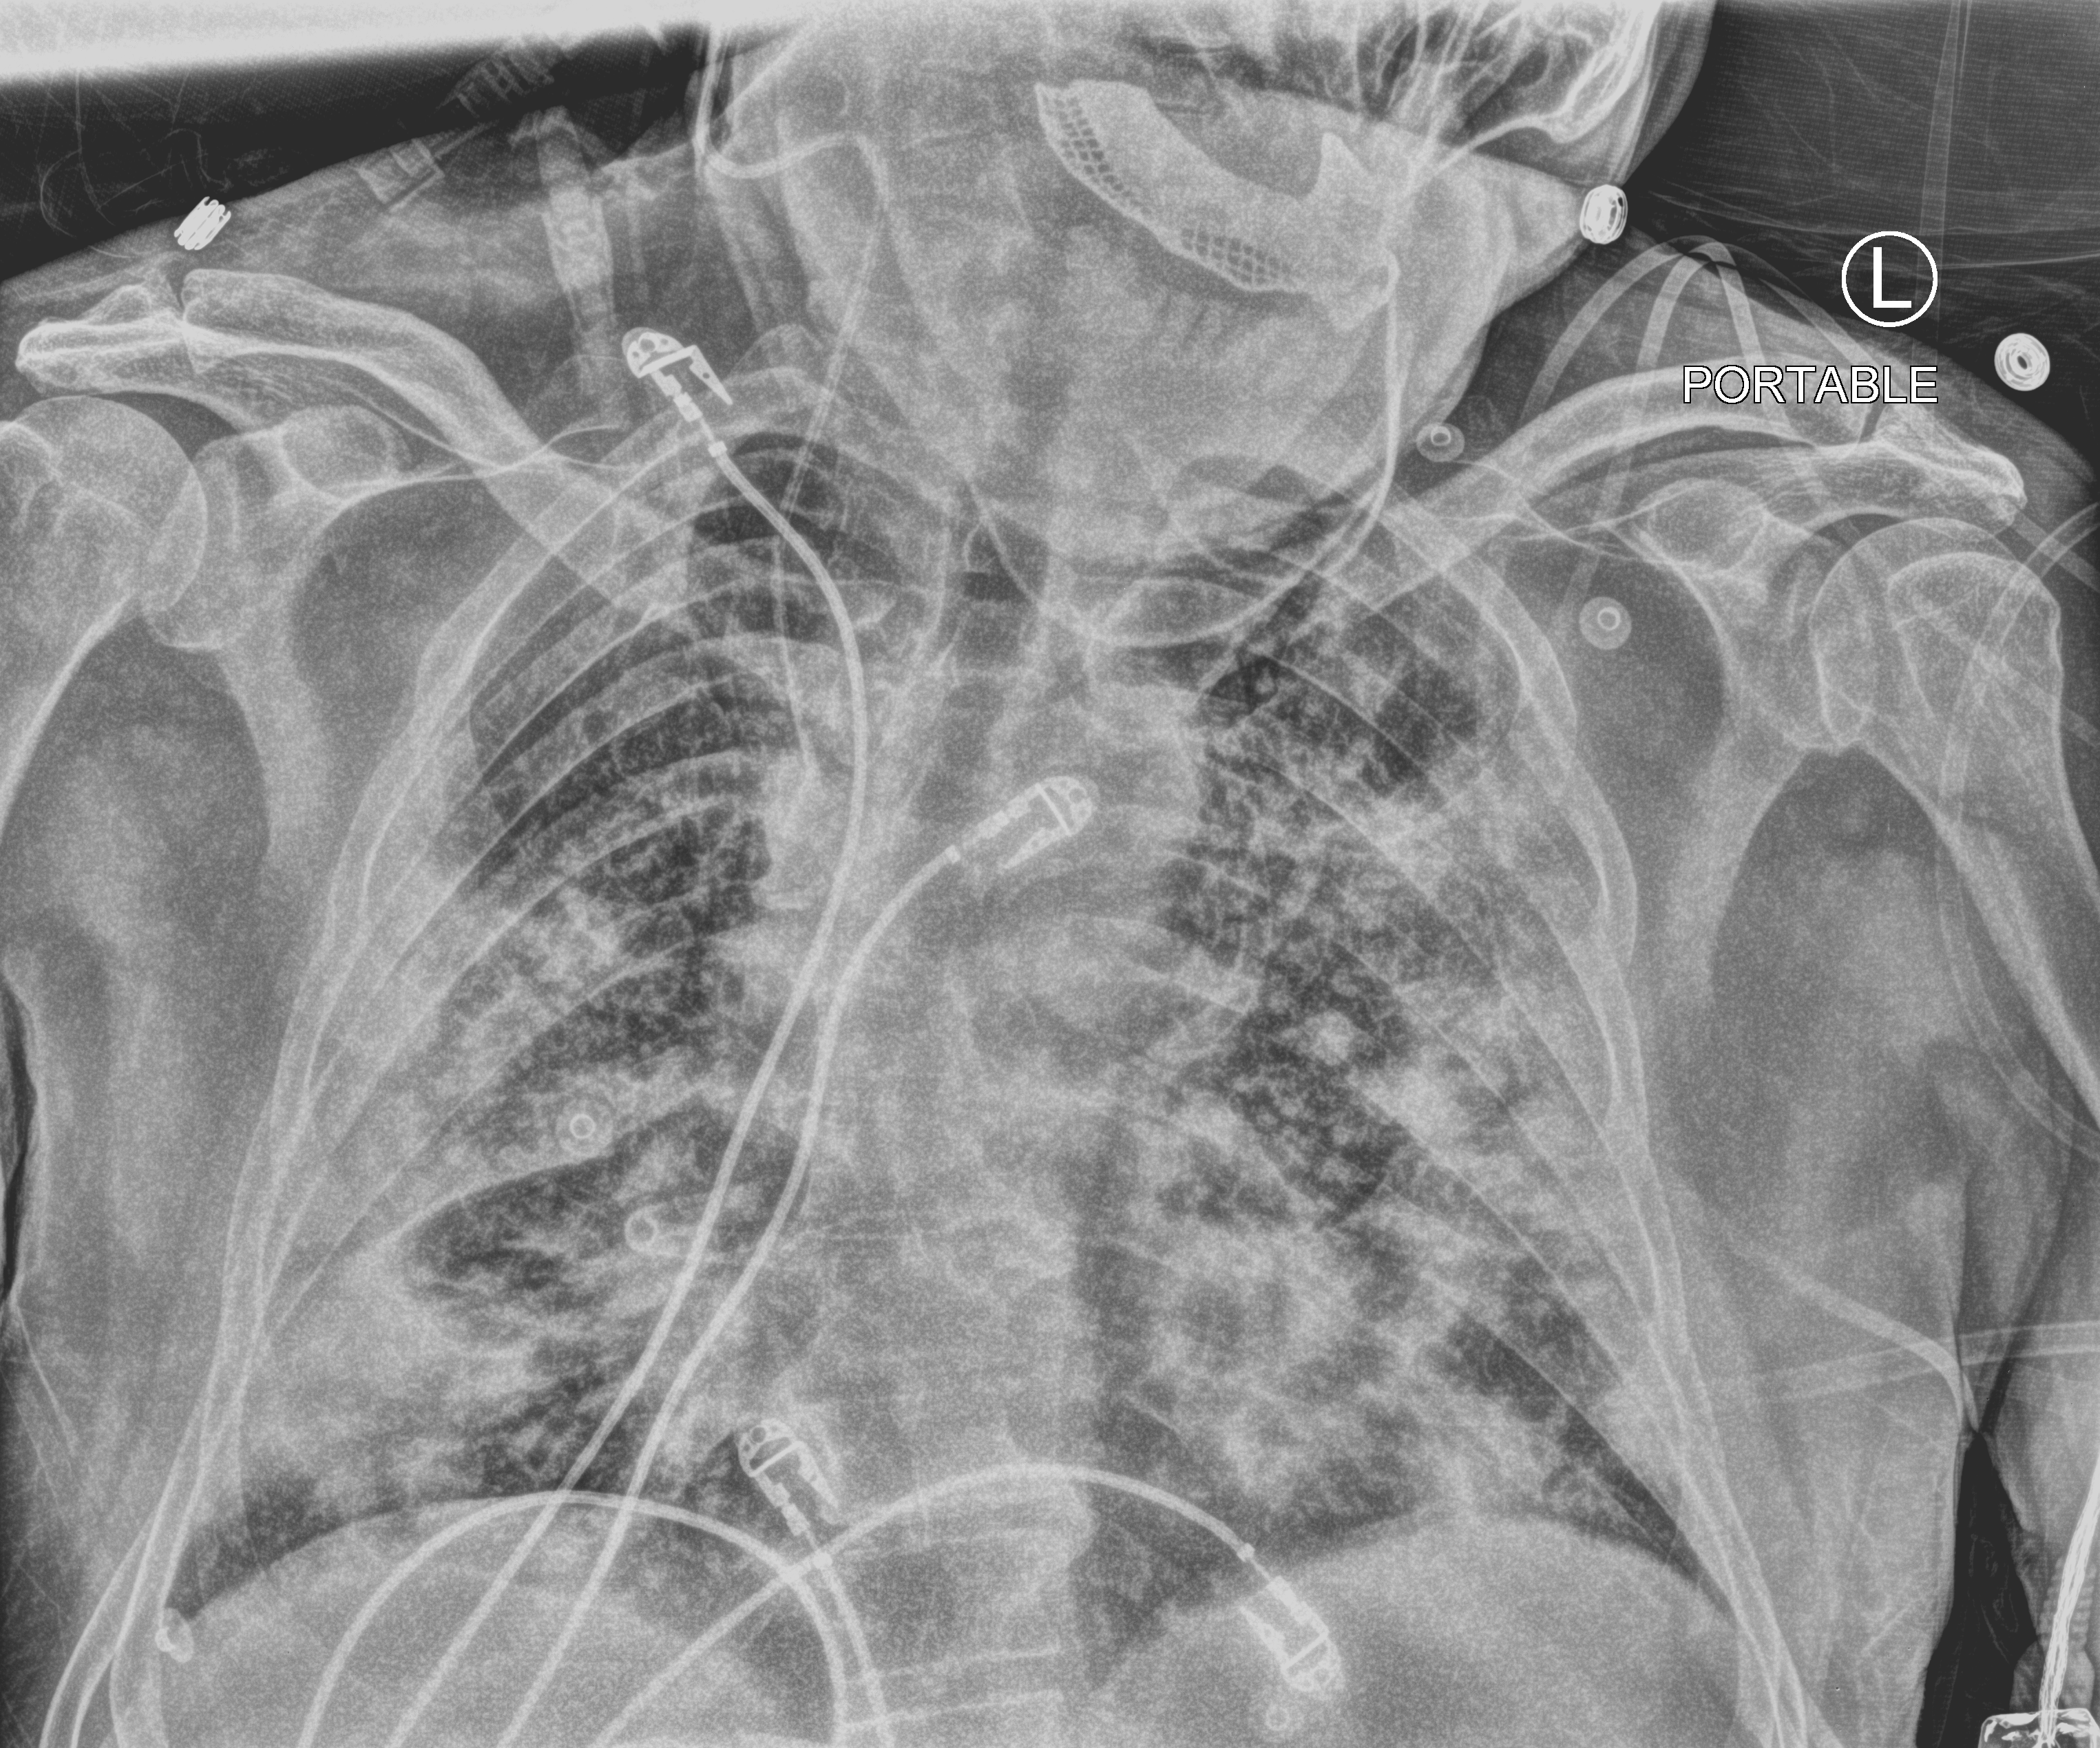
Chest X-ray (portable), anteroposterior (AP) projection. Male patient hospitalised with COVID-19, age 60–74 years.
Admission-level facts for this patient (not findings on this image; timing relative to this image not recorded):
- length of hospital stay: 32 days
- diabetes (admission record): yes